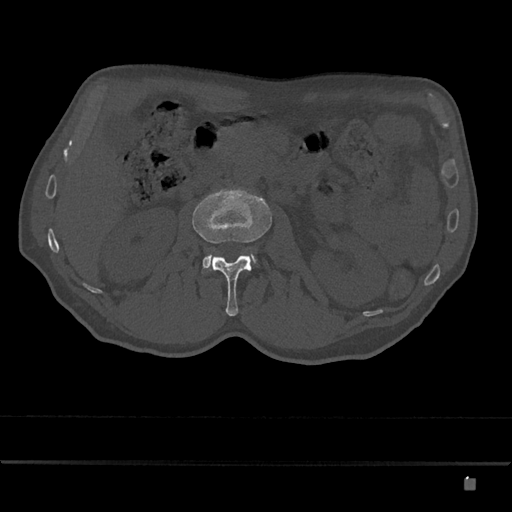
CT including the spine, one axial slice. Position 460 of 797 along the scan axis. Bone window (W 1800 / L 400 HU). 0.5 mm slice thickness. 512 × 512 image matrix, field of view 390 × 390 mm. Male patient, age 72 years. Case-level facts recorded for this patient, not image findings: primary cancer: prostate.
Annotated regions visible in this slice (semi-automatically segmented with operator editing):
- L2 vertebra: bounding box [x1, y1, x2, y2] px = [192, 188, 272, 317]
- L3 vertebra: [203, 254, 256, 269]